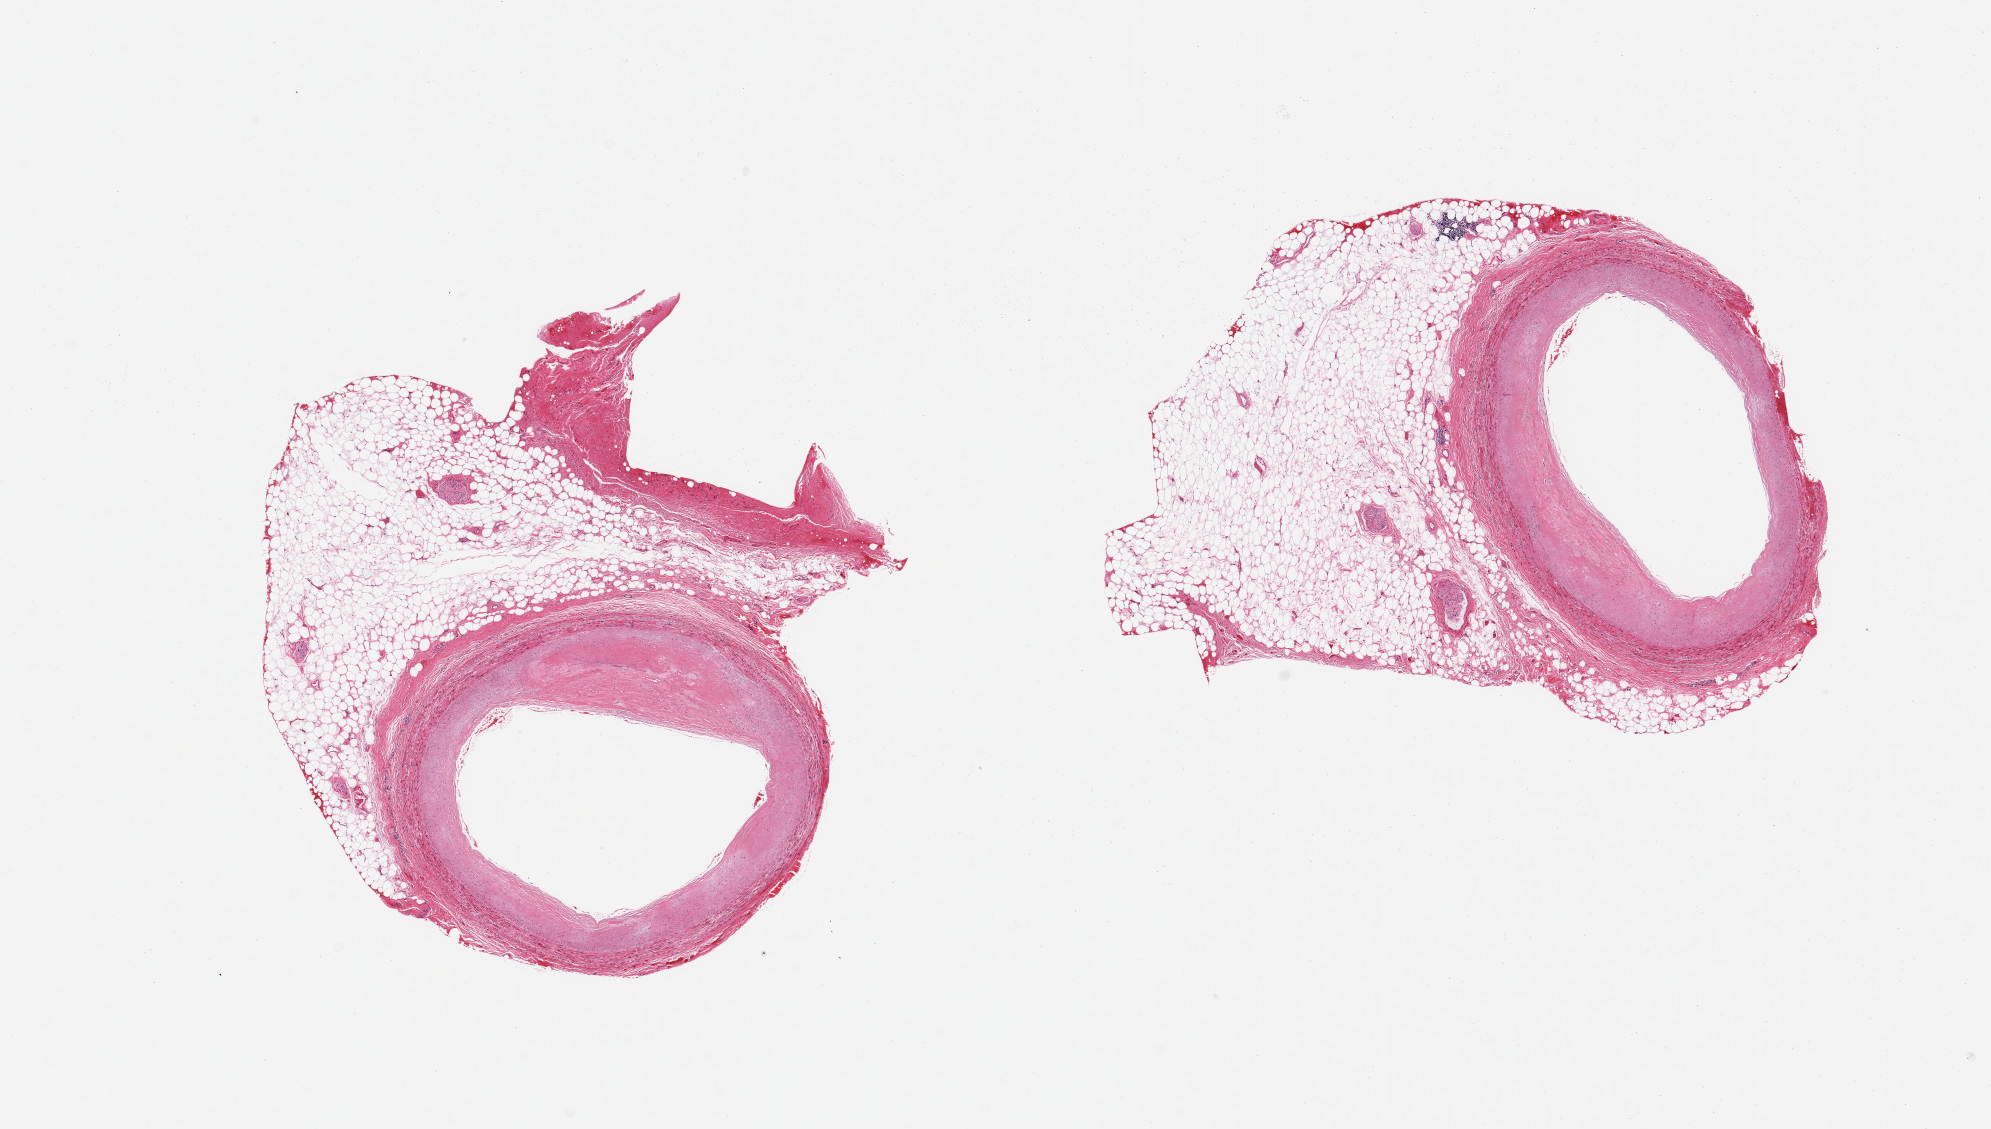
Whole-slide image, hematoxylin and eosin (H&E) stain, a low-resolution overview of the entire scanned area, about 15.8 x 8.9 mm. PAXgene-fixed paraffin-embedded (PFPE) section. Target tissue: coronary artery. Tissue donor sample. Donor: male.
• reviewer comment on this tissue sample: 2 pieces, adherent fat up to ~2.5mm, 30% tissue, ~30% occlusive atherosis